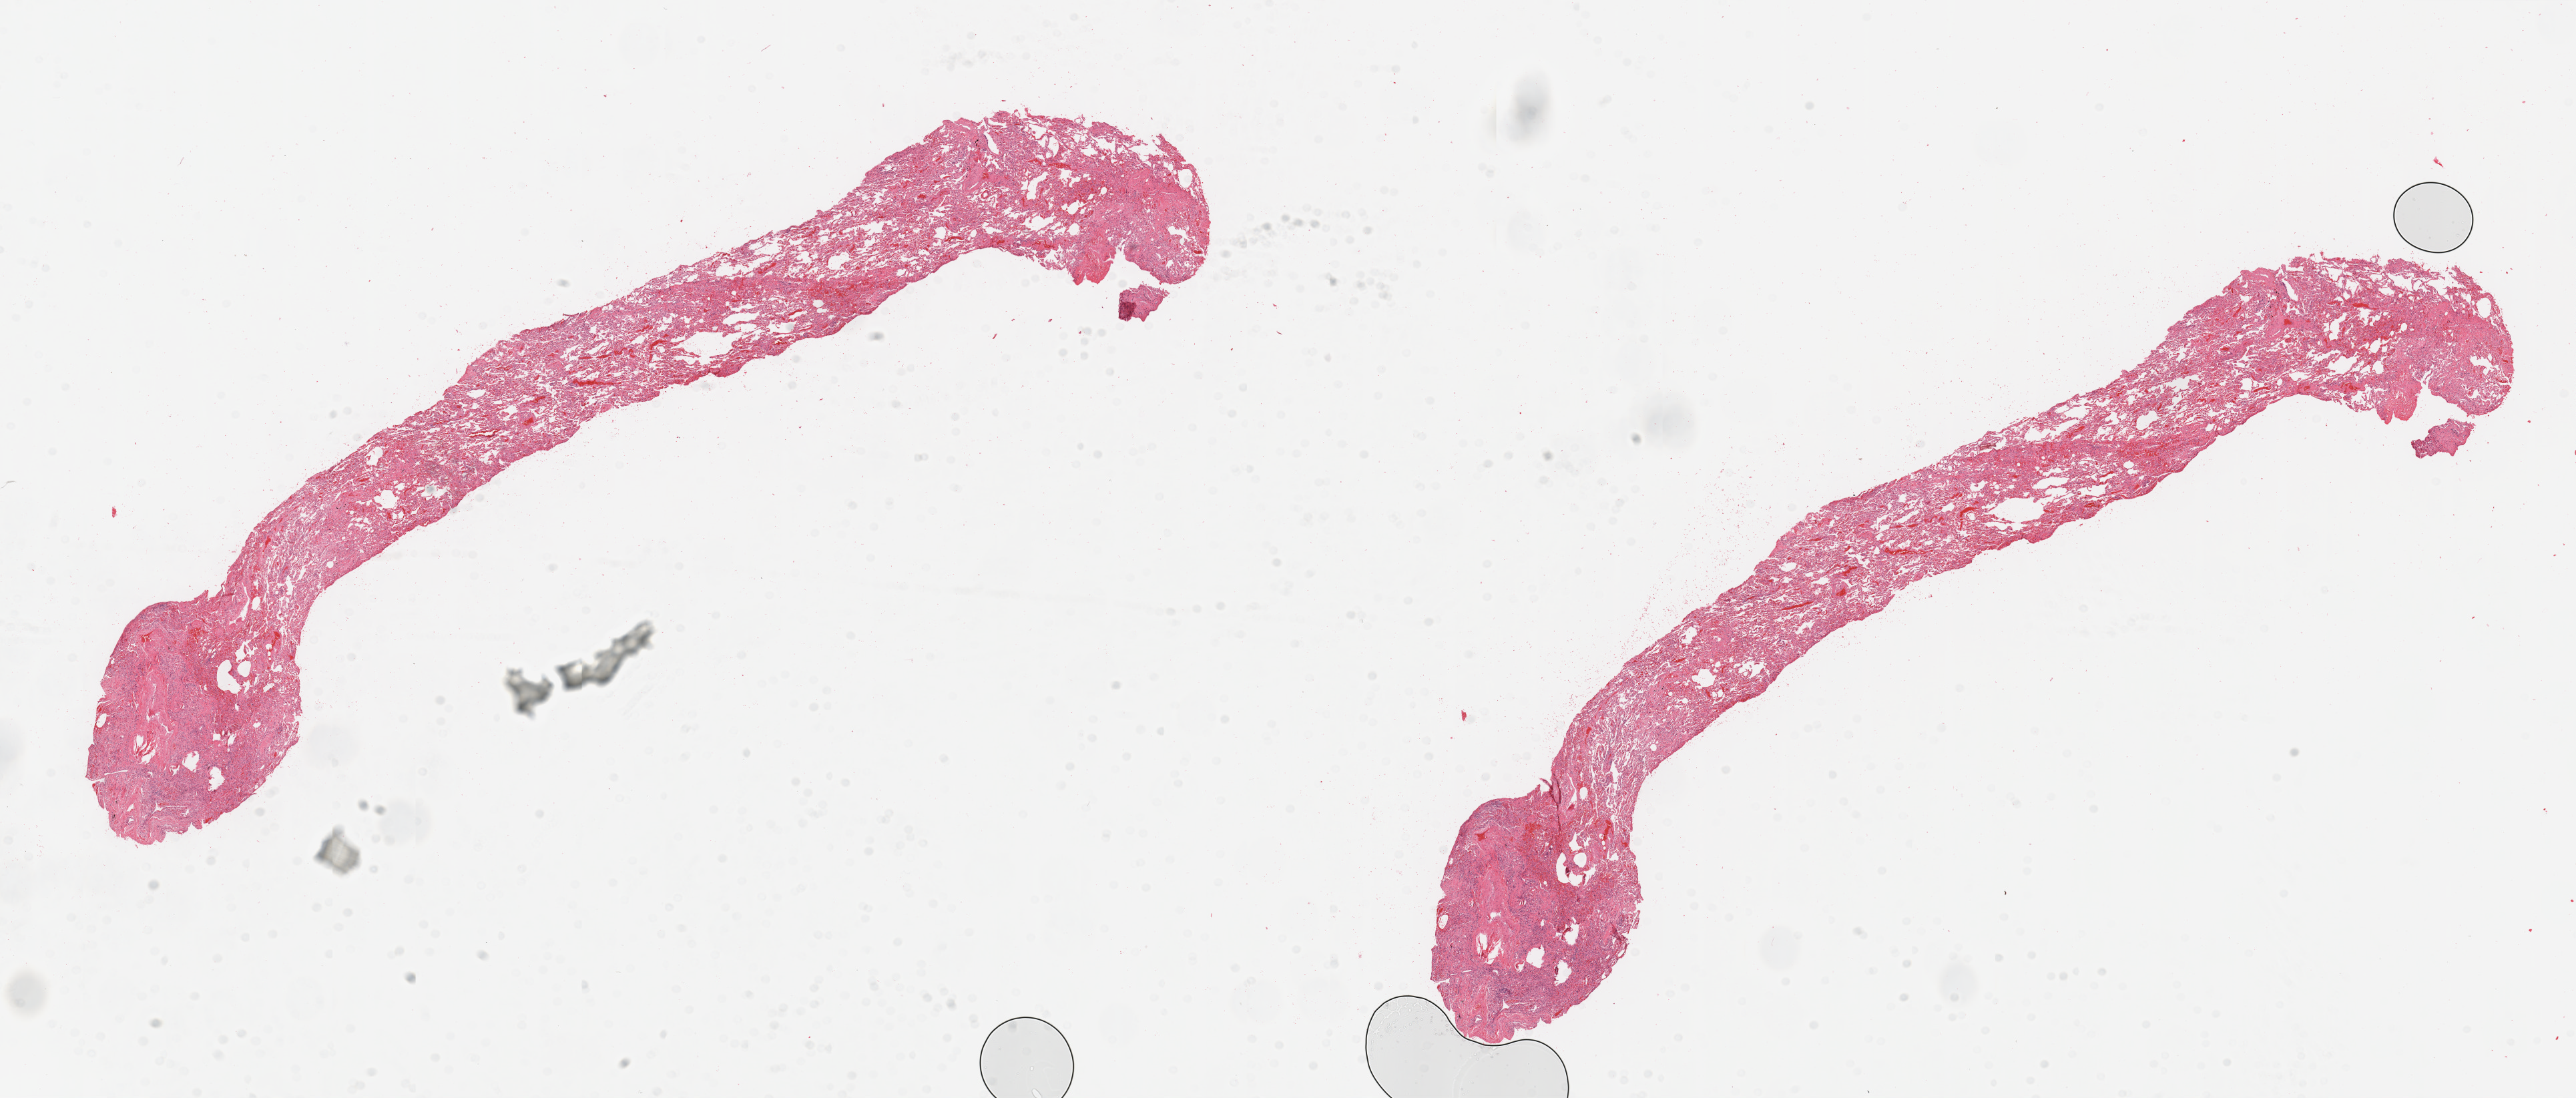
Whole-slide histology image, H&E-stained — a low-resolution overview of the entire scanned area, about 30.5 x 13.0 mm (from a 20x scan), normal (non-tumour) tissue sample, lung. Male, 65 y/o.
This section: normal (non-tumour) tissue from the same patient. Patient diagnosis: Adenocarcinoma, NOS.